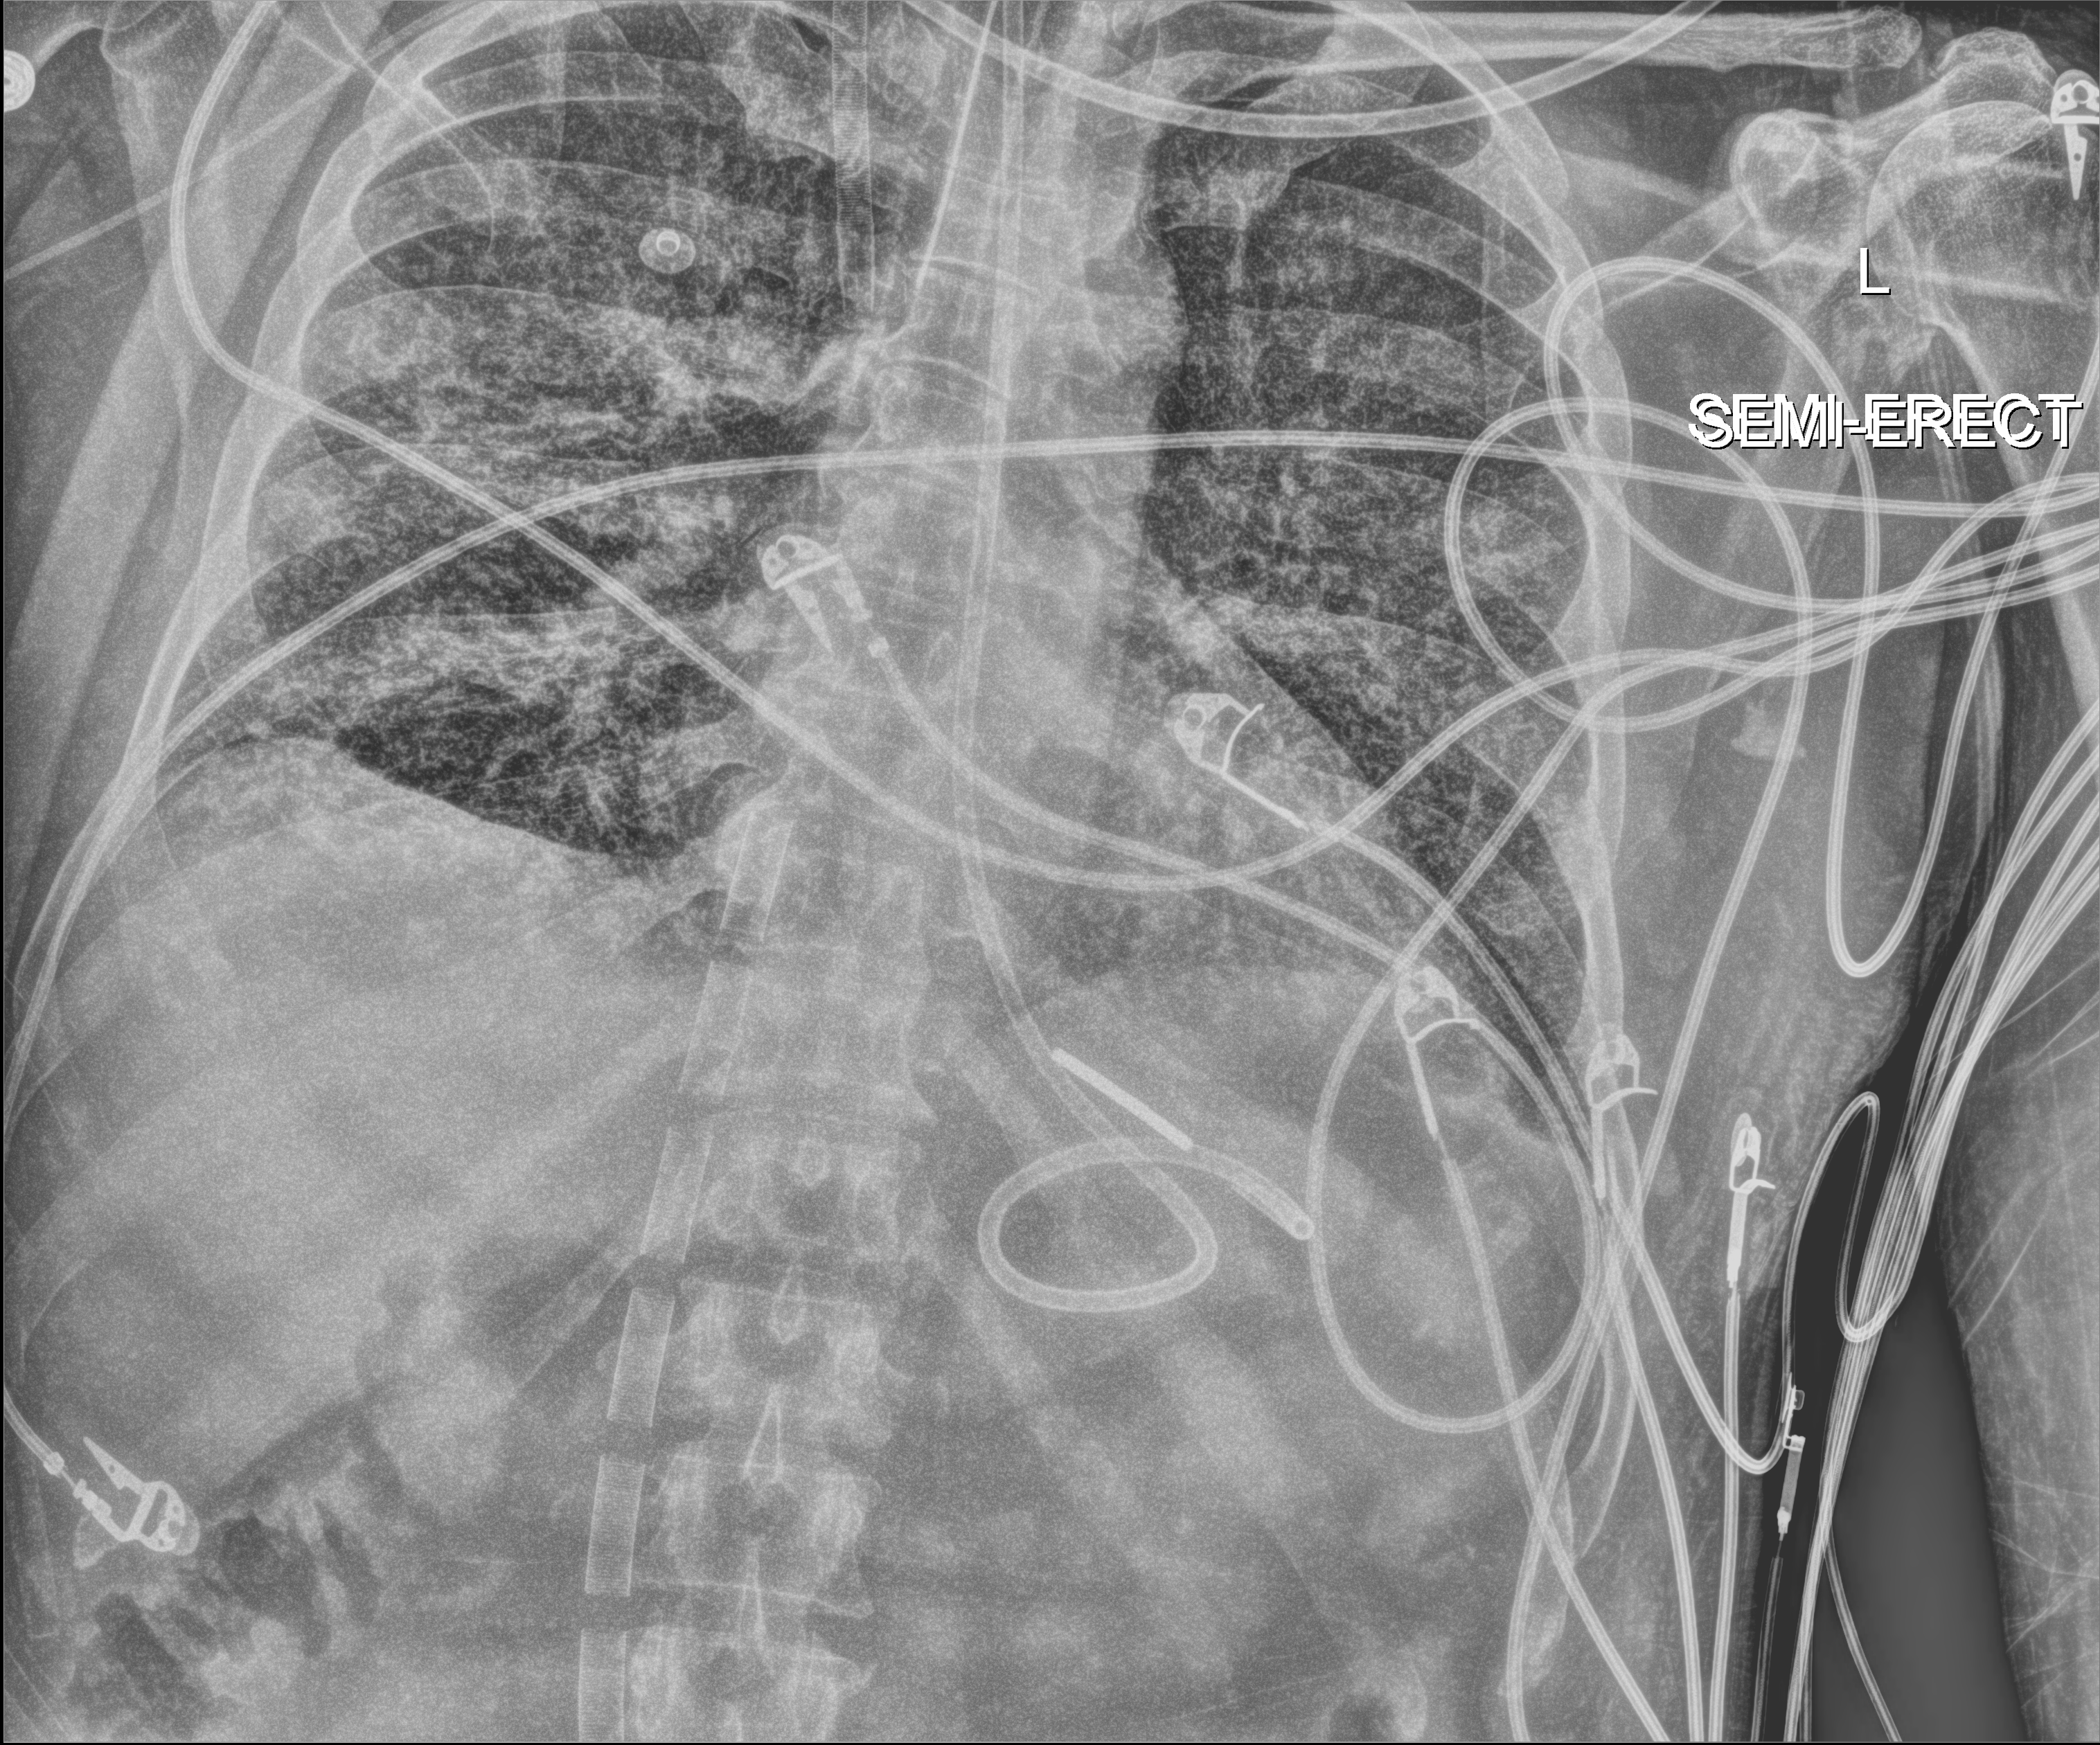
Bedside chest radiograph (digital radiography); anteroposterior (AP) projection. Patient hospitalised with COVID-19; male, aged 18–59 years.
Hospital-stay facts (about this admission, not read from this image; timing relative to this image not recorded): mechanically ventilated during this hospital stay: yes; hypertension (admission record): no.